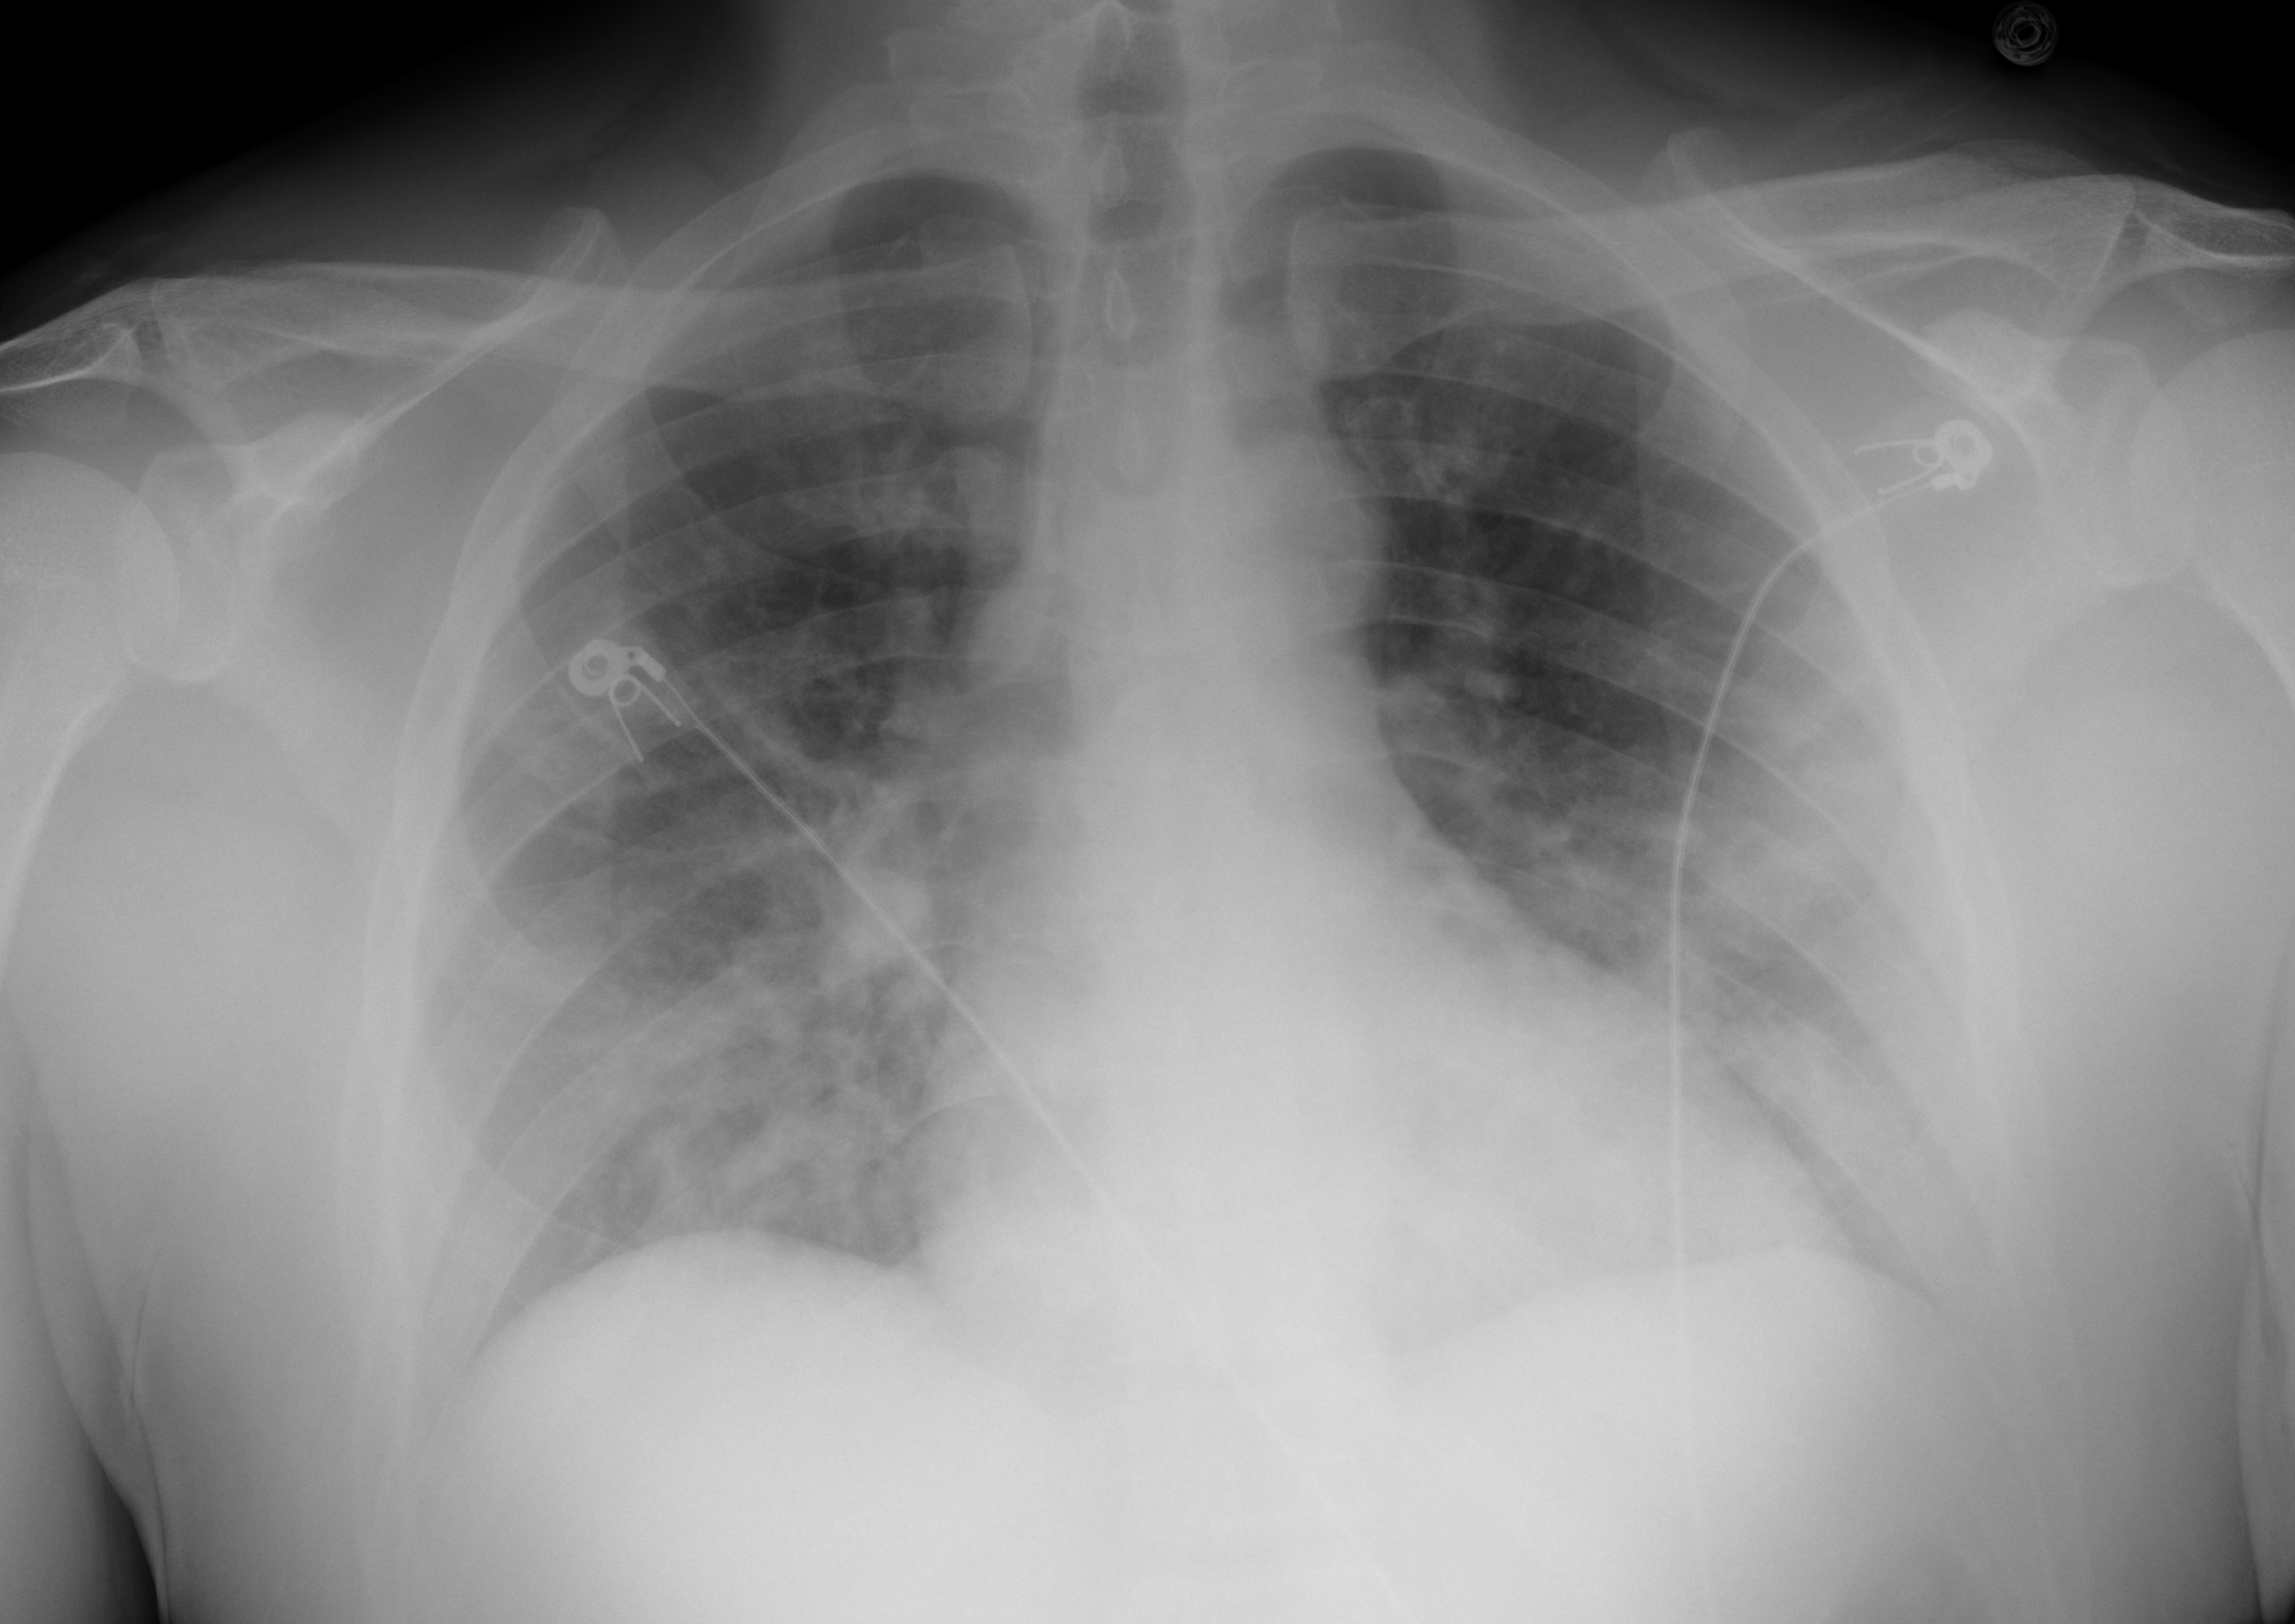
Portable chest radiograph, AP projection. Male patient, age 48 years; COVID-19 (test-positive).
Radiologist's key findings for this exam: Patchy bilateral ground-glass/consolidative opacities are seen in the bilateral lung bases.